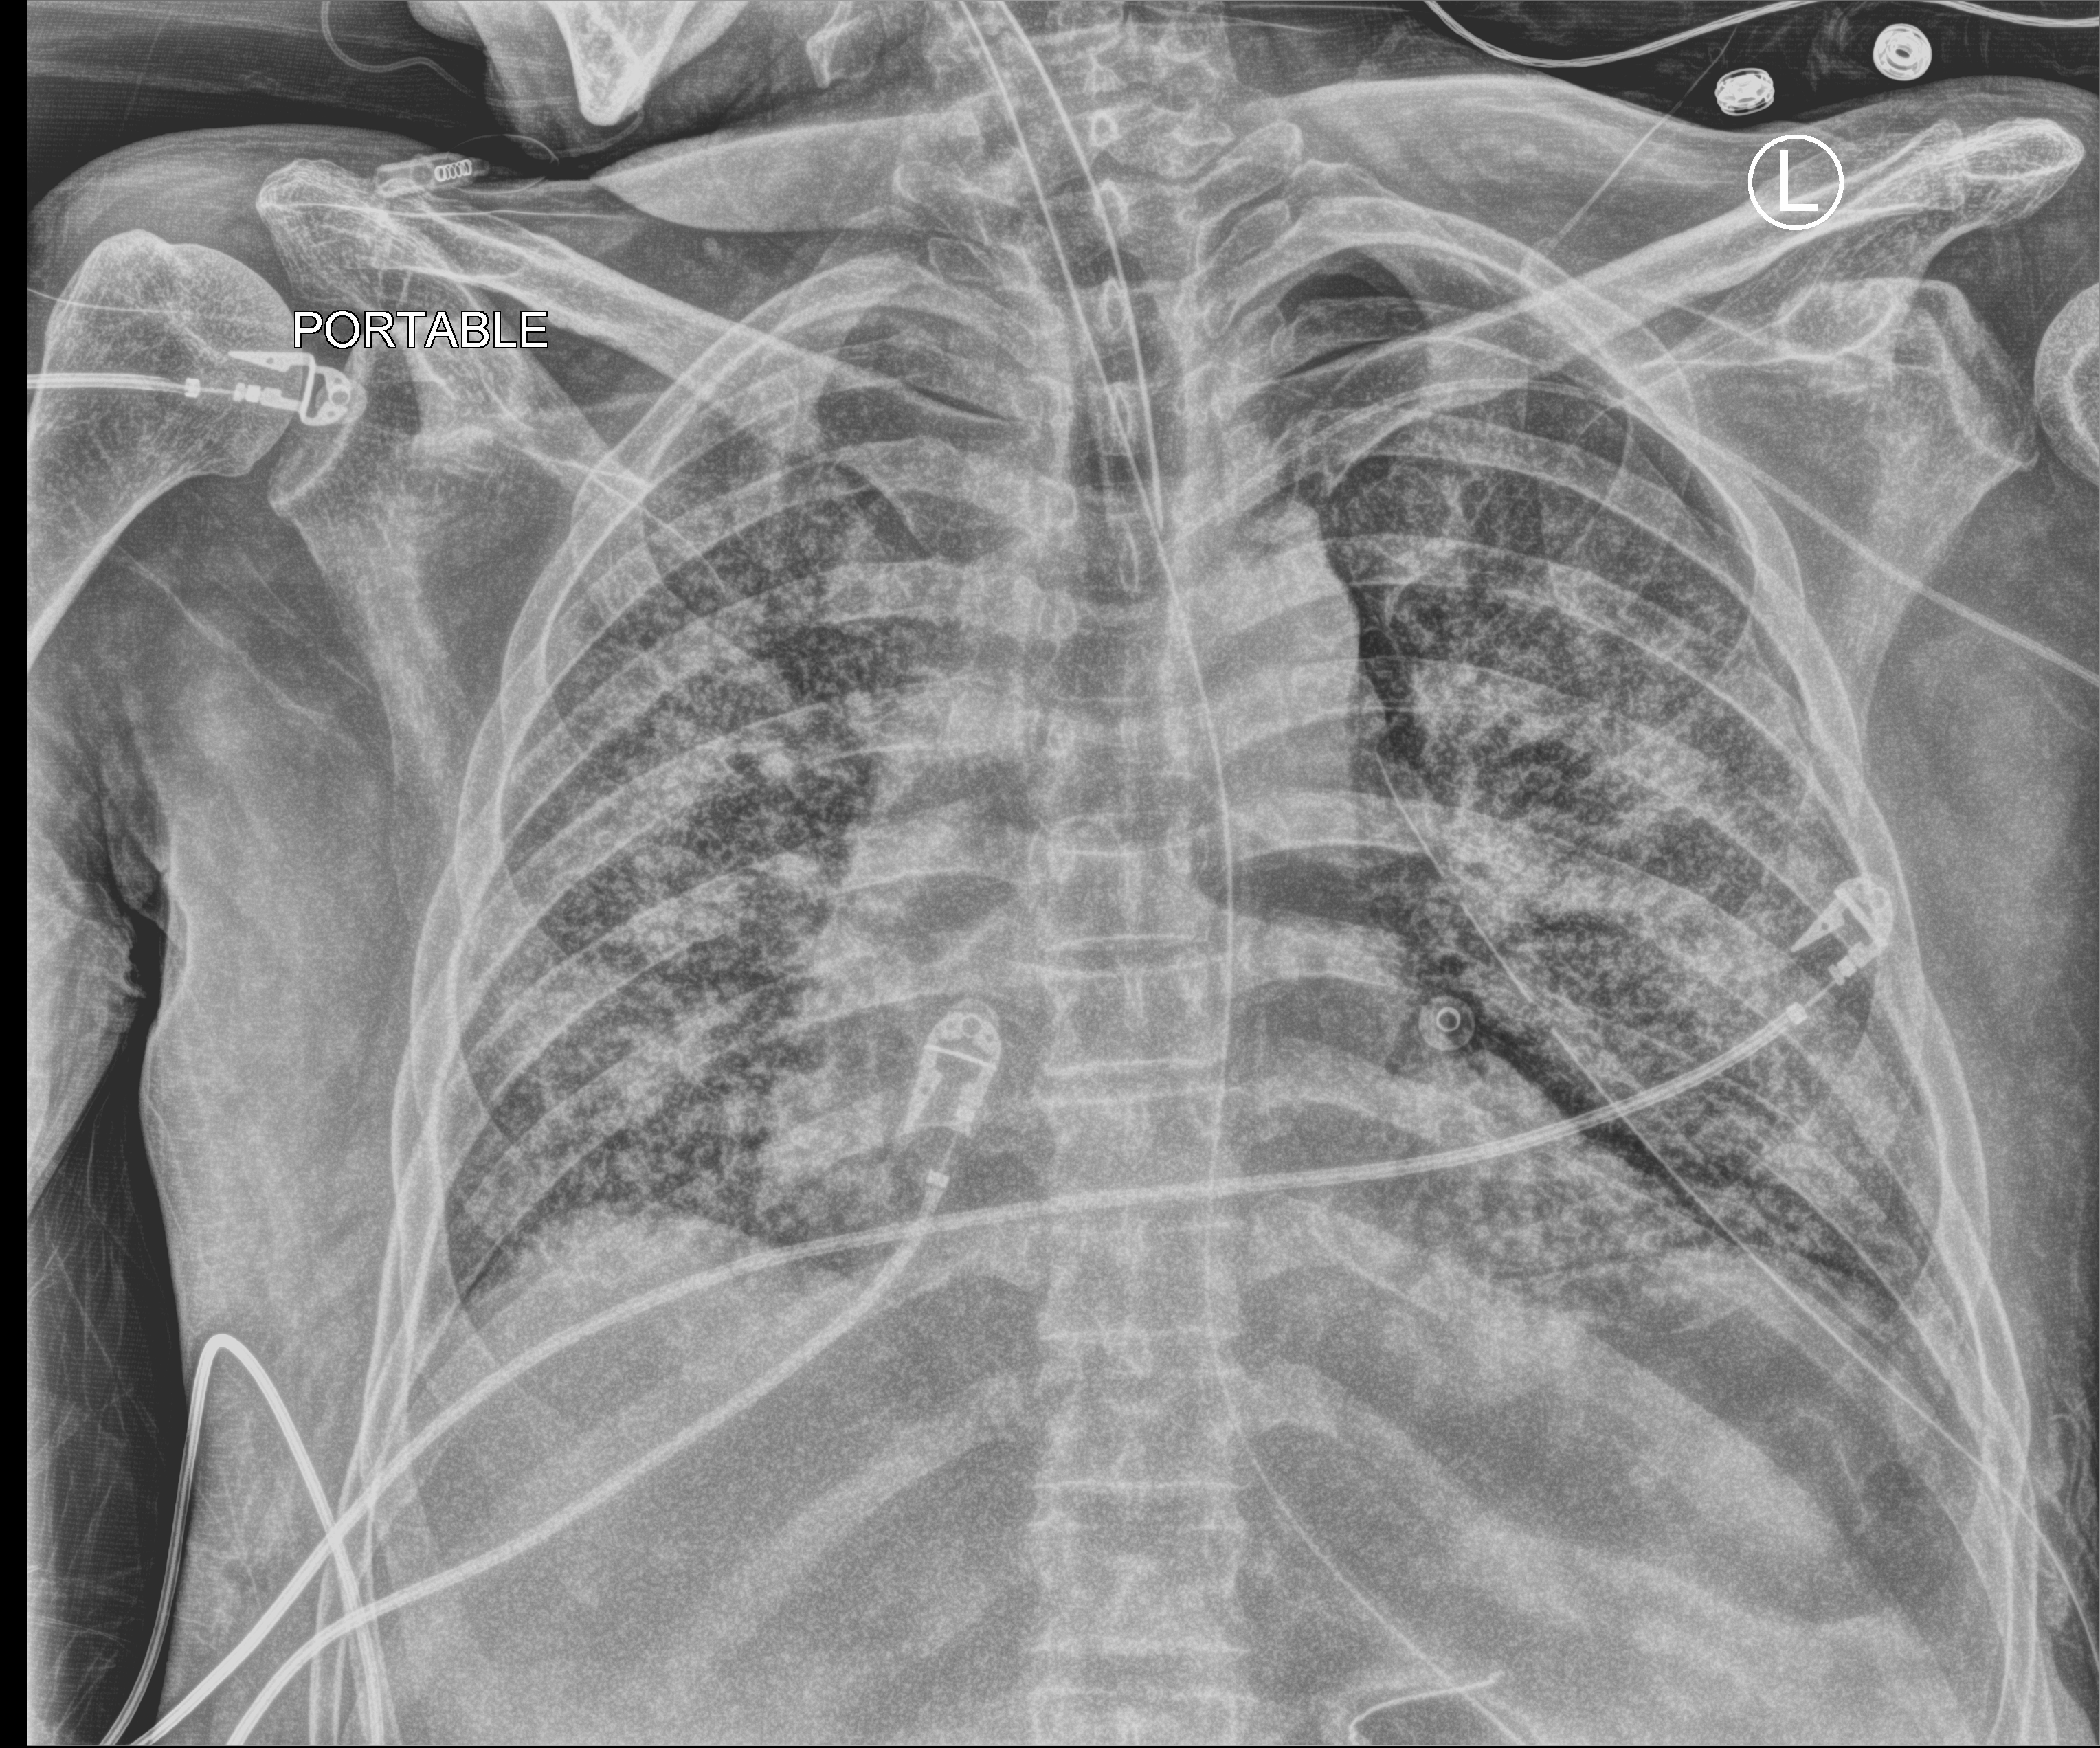
Bedside chest radiograph (computed radiography), anteroposterior (AP) projection. Male patient hospitalised with COVID-19, age 60–74 years.
Admission-level facts for this patient (not findings on this image; timing relative to this image not recorded): admitted to intensive care during this hospital stay: yes.